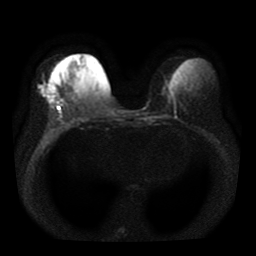
Breast MRI, one axial slice. Diffusion-weighted series; image 2 of 4 stored at this slice position (different b-values; order by instance number). 1.5 T. 5 mm slice thickness. 256 × 256 image matrix, field of view 330 × 330 mm. Female patient.
Annotated regions visible in this slice (expert manual segmentation):
- tumour on diffusion-weighted imaging: bounding box [x1, y1, x2, y2] px = [41, 85, 55, 100]